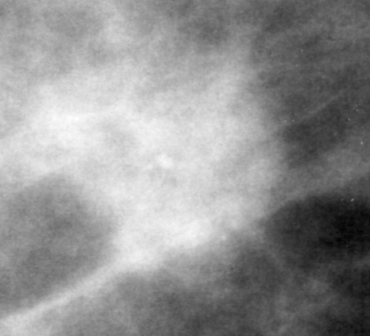
Region of interest cut from a scanned film mammogram (one marked finding), left breast, CC view, BI-RADS breast density category 4 (scale 1–4).
Finding: mass, shape focal asymmetric density, margins ill defined; BI-RADS assessment category 4; subtlety rating 3 on a 1 (subtle) to 5 (obvious) scale; pathology result (as recorded, not read from the image): malignant.